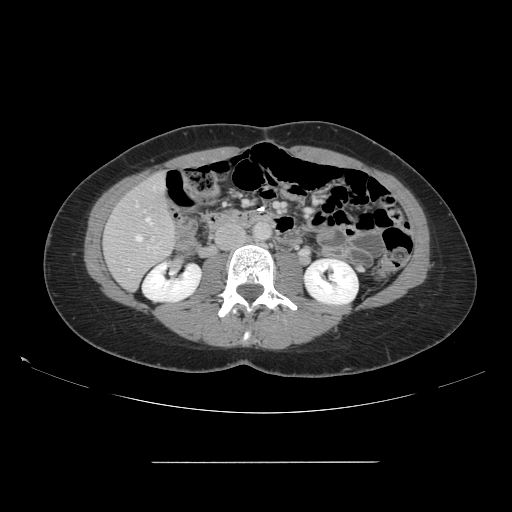
Contrast-enhanced abdominal CT, one axial slice; position 49 of 151 along the scan axis; 120 kVp; intravenous contrast given; soft-tissue window (W 400 / L 40 HU); 512 × 512 image matrix, field of view 421 × 421 mm. Female patient, age 46 years. From the clinical record (not read from this slice): diagnosis: colorectal cancer liver metastases, imaged before liver resection; multiple liver metastases: yes; largest metastasis: 3 cm; chemotherapy before resection: no.
Structures marked on this image (manually delineated by an expert):
- hepatic veins: bounding box <136,218,151,241> (left, top, right, bottom; pixels)
- liver: <105,174,176,289>
- planned liver remnant (the part of the liver to remain after resection): <105,175,176,289>